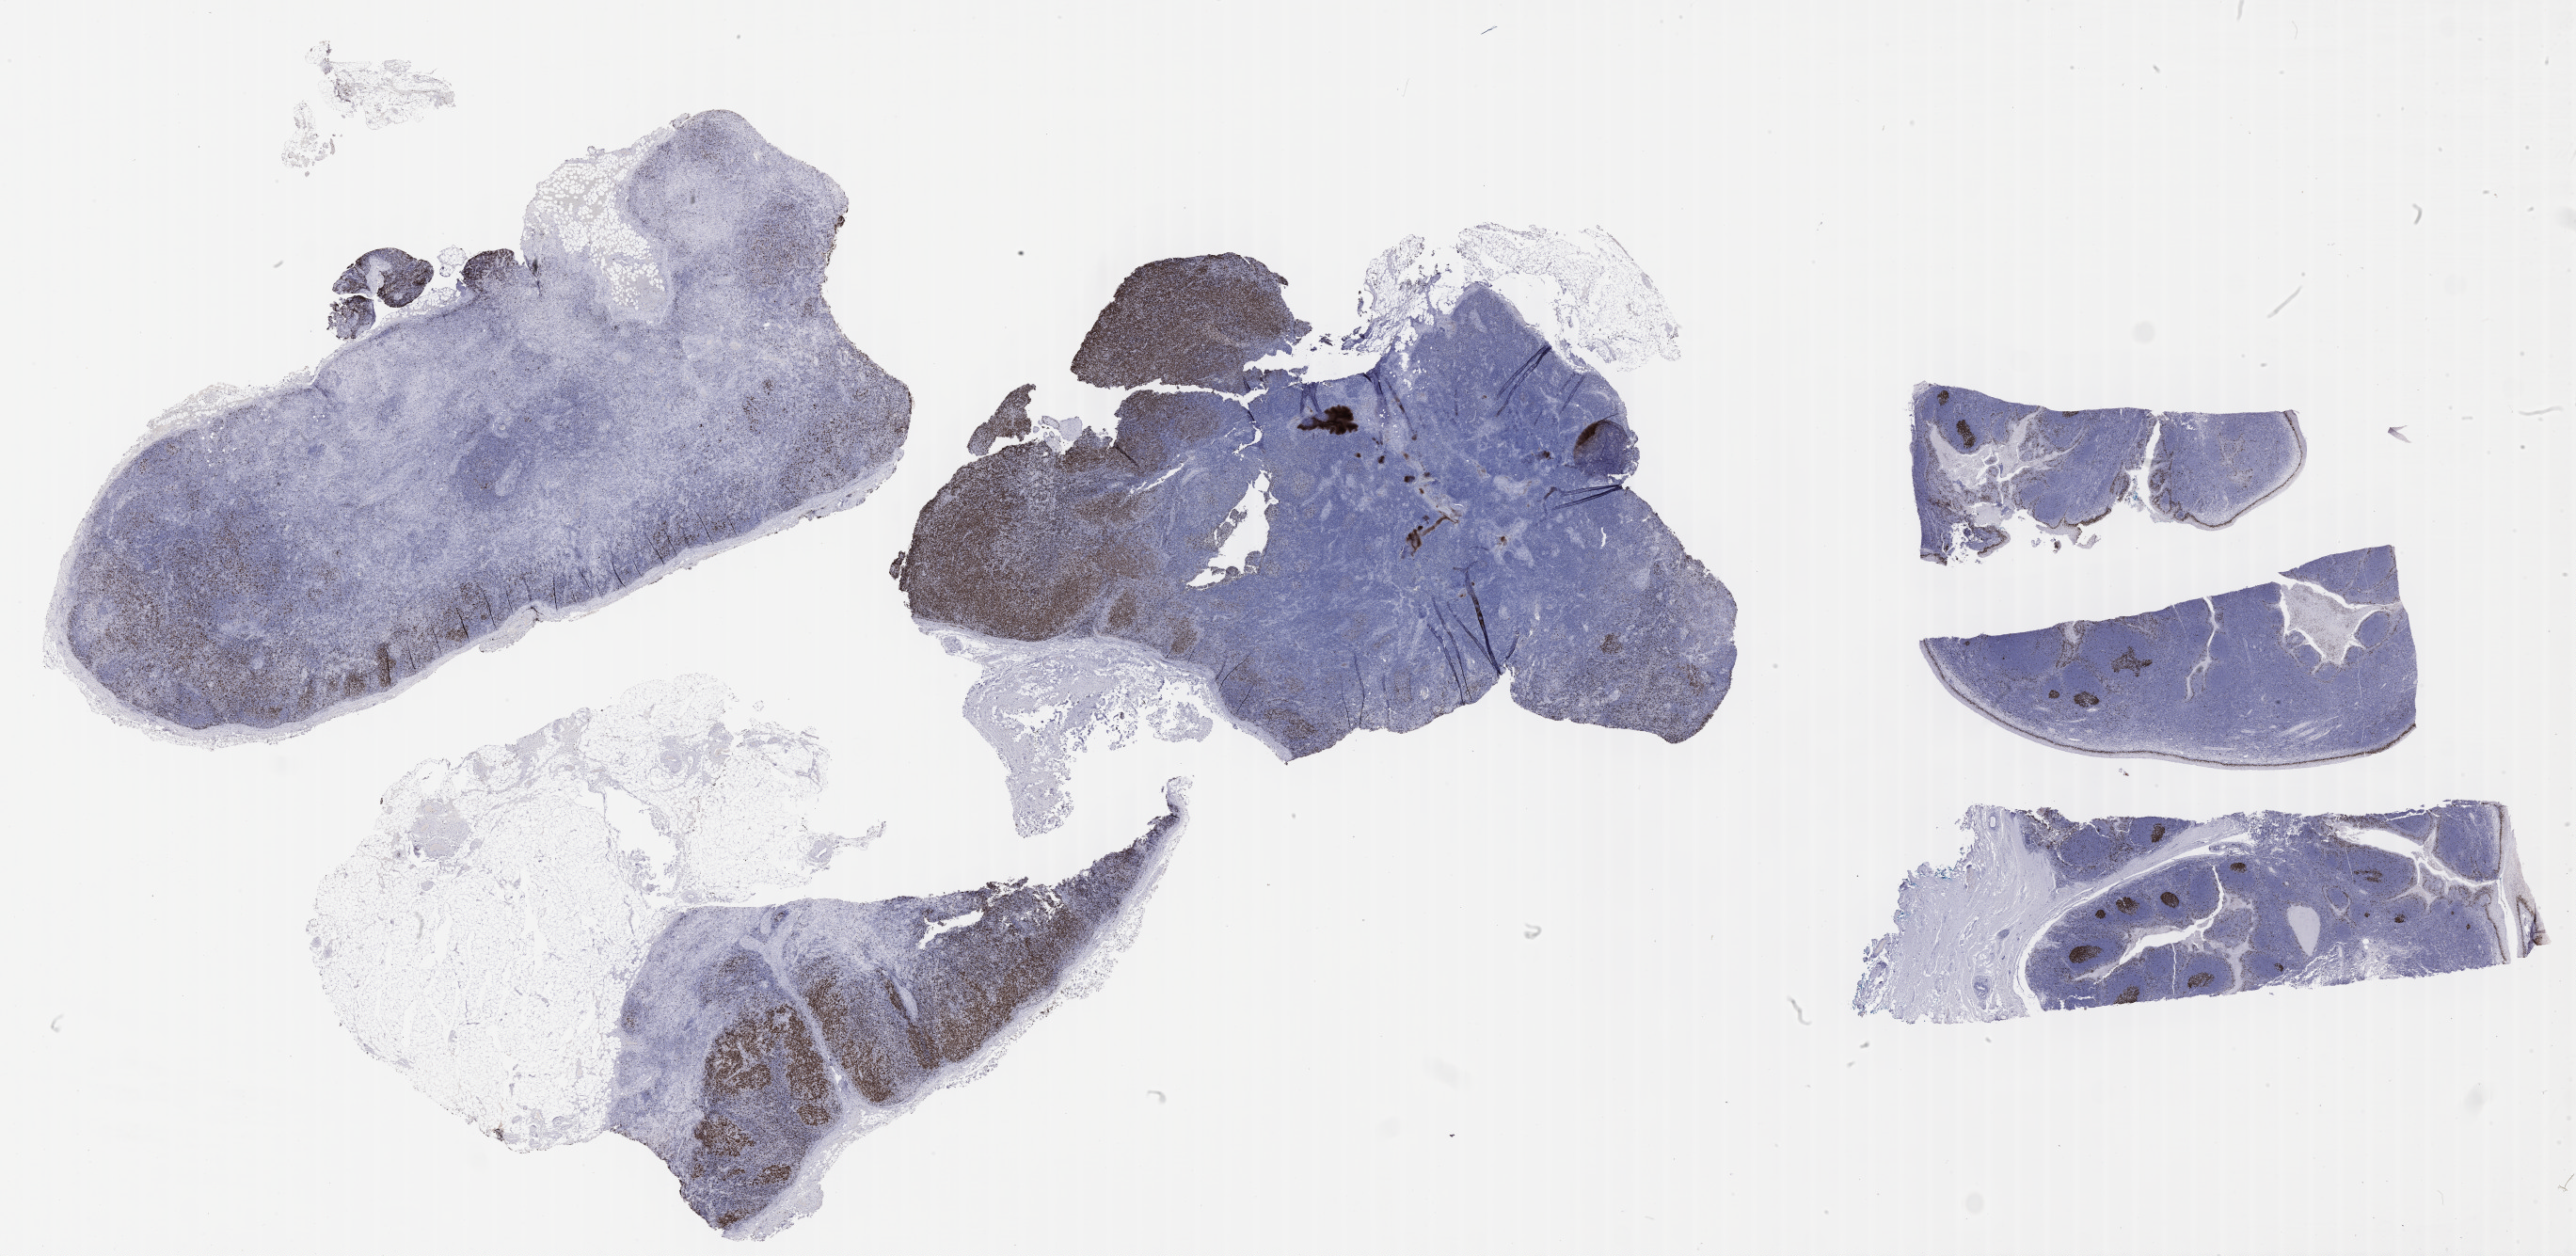
Whole-slide image, immunohistochemical stain for Ki-67 — a low-resolution overview of the entire scanned area, about 44.3 x 21.6 mm; specimen: tumor tissue; anatomic site: lymph node. Patient: male, 56 years old.
• diagnosis: Diffuse large B-cell lymphoma, NOS